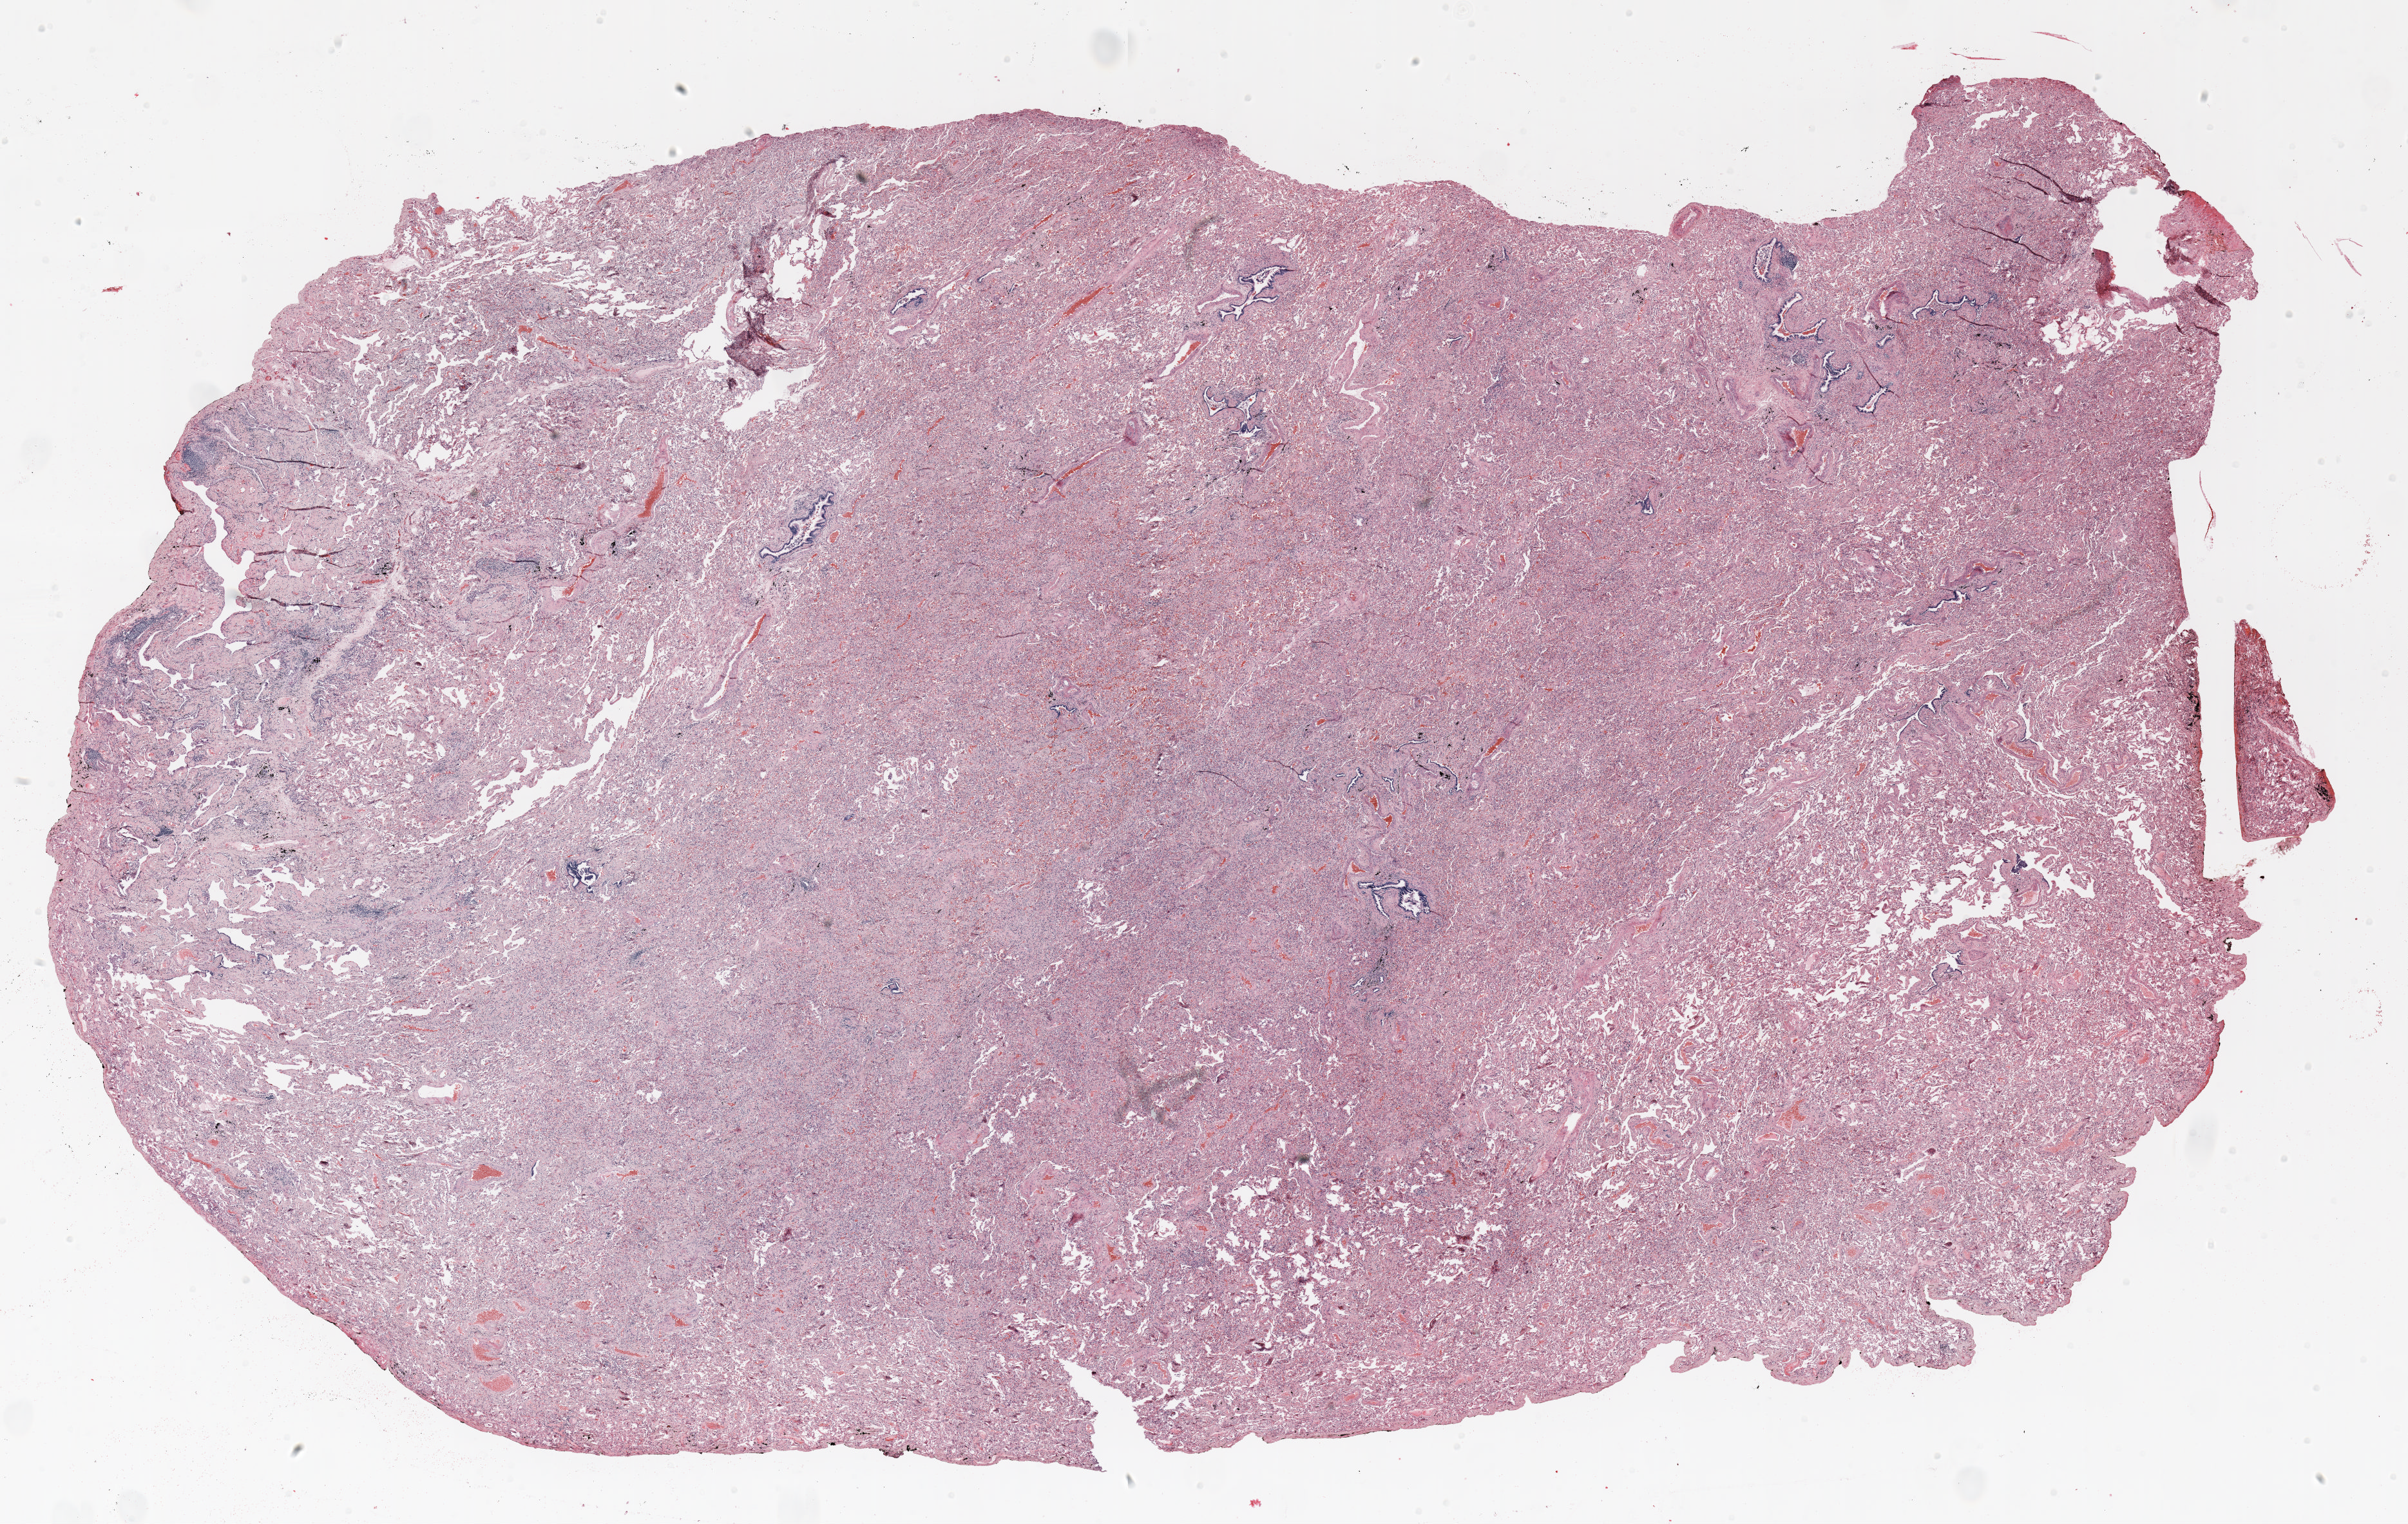
Whole-slide histology image, H&E, a low-resolution overview of the entire scanned area, about 30.0 x 19.0 mm. Formalin-fixed paraffin-embedded (FFPE) section. Lung. Female, age 67 at enrolment. Former smoker at enrolment.
Participant's lung-cancer diagnosis: Adenocarcinoma, NOS.